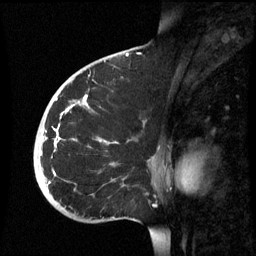
Breast MRI (dynamic contrast-enhanced), one sagittal slice; slice 36 of 60 in the series (ordered by position); dynamic contrast-enhanced series, image 2 of 3 at this slice position (ordered by acquisition); 1.5 T; TE 4.2 ms, TR 8.9 ms; 2.6 mm slice thickness; 256 × 256 image matrix. Patient: female, 35 years. From the clinical record (not read from this slice): setting: breast cancer imaged before/during neoadjuvant chemotherapy; receptor status: HR-positive, HER2-negative.
Outlined on this slice (semi-automatic segmentation, software-assisted and operator-edited):
- analysis volume of interest (the breast-tissue region the enhancement analysis was run in; not a lesion): bounding box (x1, y1, x2, y2) in pixels: (34, 74, 161, 221)
- tumour enhancement mask (voxels above the 70 % enhancement threshold inside the analysis volume of interest): (53, 96, 101, 173)